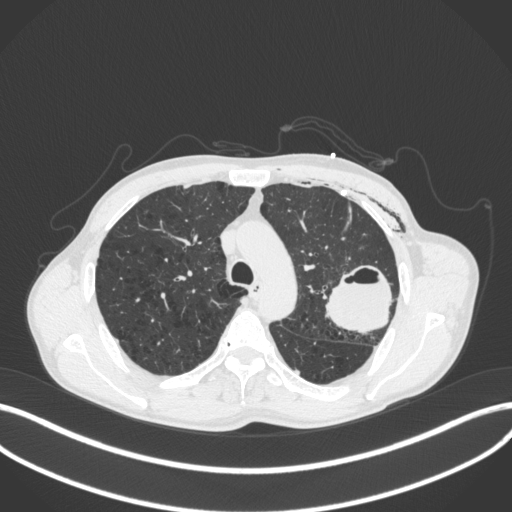
Chest CT, one axial slice; position 289 of 416 along the scan axis; reconstruction kernel B31f; 120 kVp; lung window (W 1500 / L -600 HU); 512 × 512 image matrix, field of view 400 × 400 mm. Male patient, age 58 years. Case-level facts recorded for this patient, not image findings: clinical TNM (as recorded): T3 N0 M0.
Structures marked on this image (bounding box drawn by a radiologist):
- lung tumour (recorded histology: adenocarcinoma): bounding box [x1, y1, x2, y2] px = [324, 266, 394, 338]